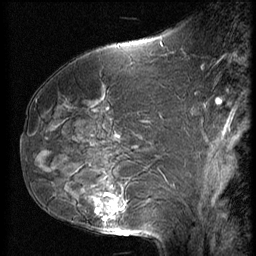
Breast MRI (dynamic contrast-enhanced), one sagittal slice; 3 images stored at this slice position (order not interpretable as contrast timing); 1.5 T; TE 4.2 ms, TR 9 ms; 2.5 mm slice thickness; 256 × 256 image matrix. Patient: female, 50 years. From the clinical record (not read from this slice): setting: breast cancer imaged before/during neoadjuvant chemotherapy; receptor status: HR-positive, HER2-negative.
Outlined on this slice (semi-automatically segmented with operator editing):
- analysis volume of interest (the breast-tissue region the enhancement analysis was run in; not a lesion): box from (x=59, y=125) to (x=139, y=237) px
- tumour enhancement mask (voxels above the 140 % enhancement threshold inside the analysis volume of interest): (x=96, y=193)–(x=117, y=221)